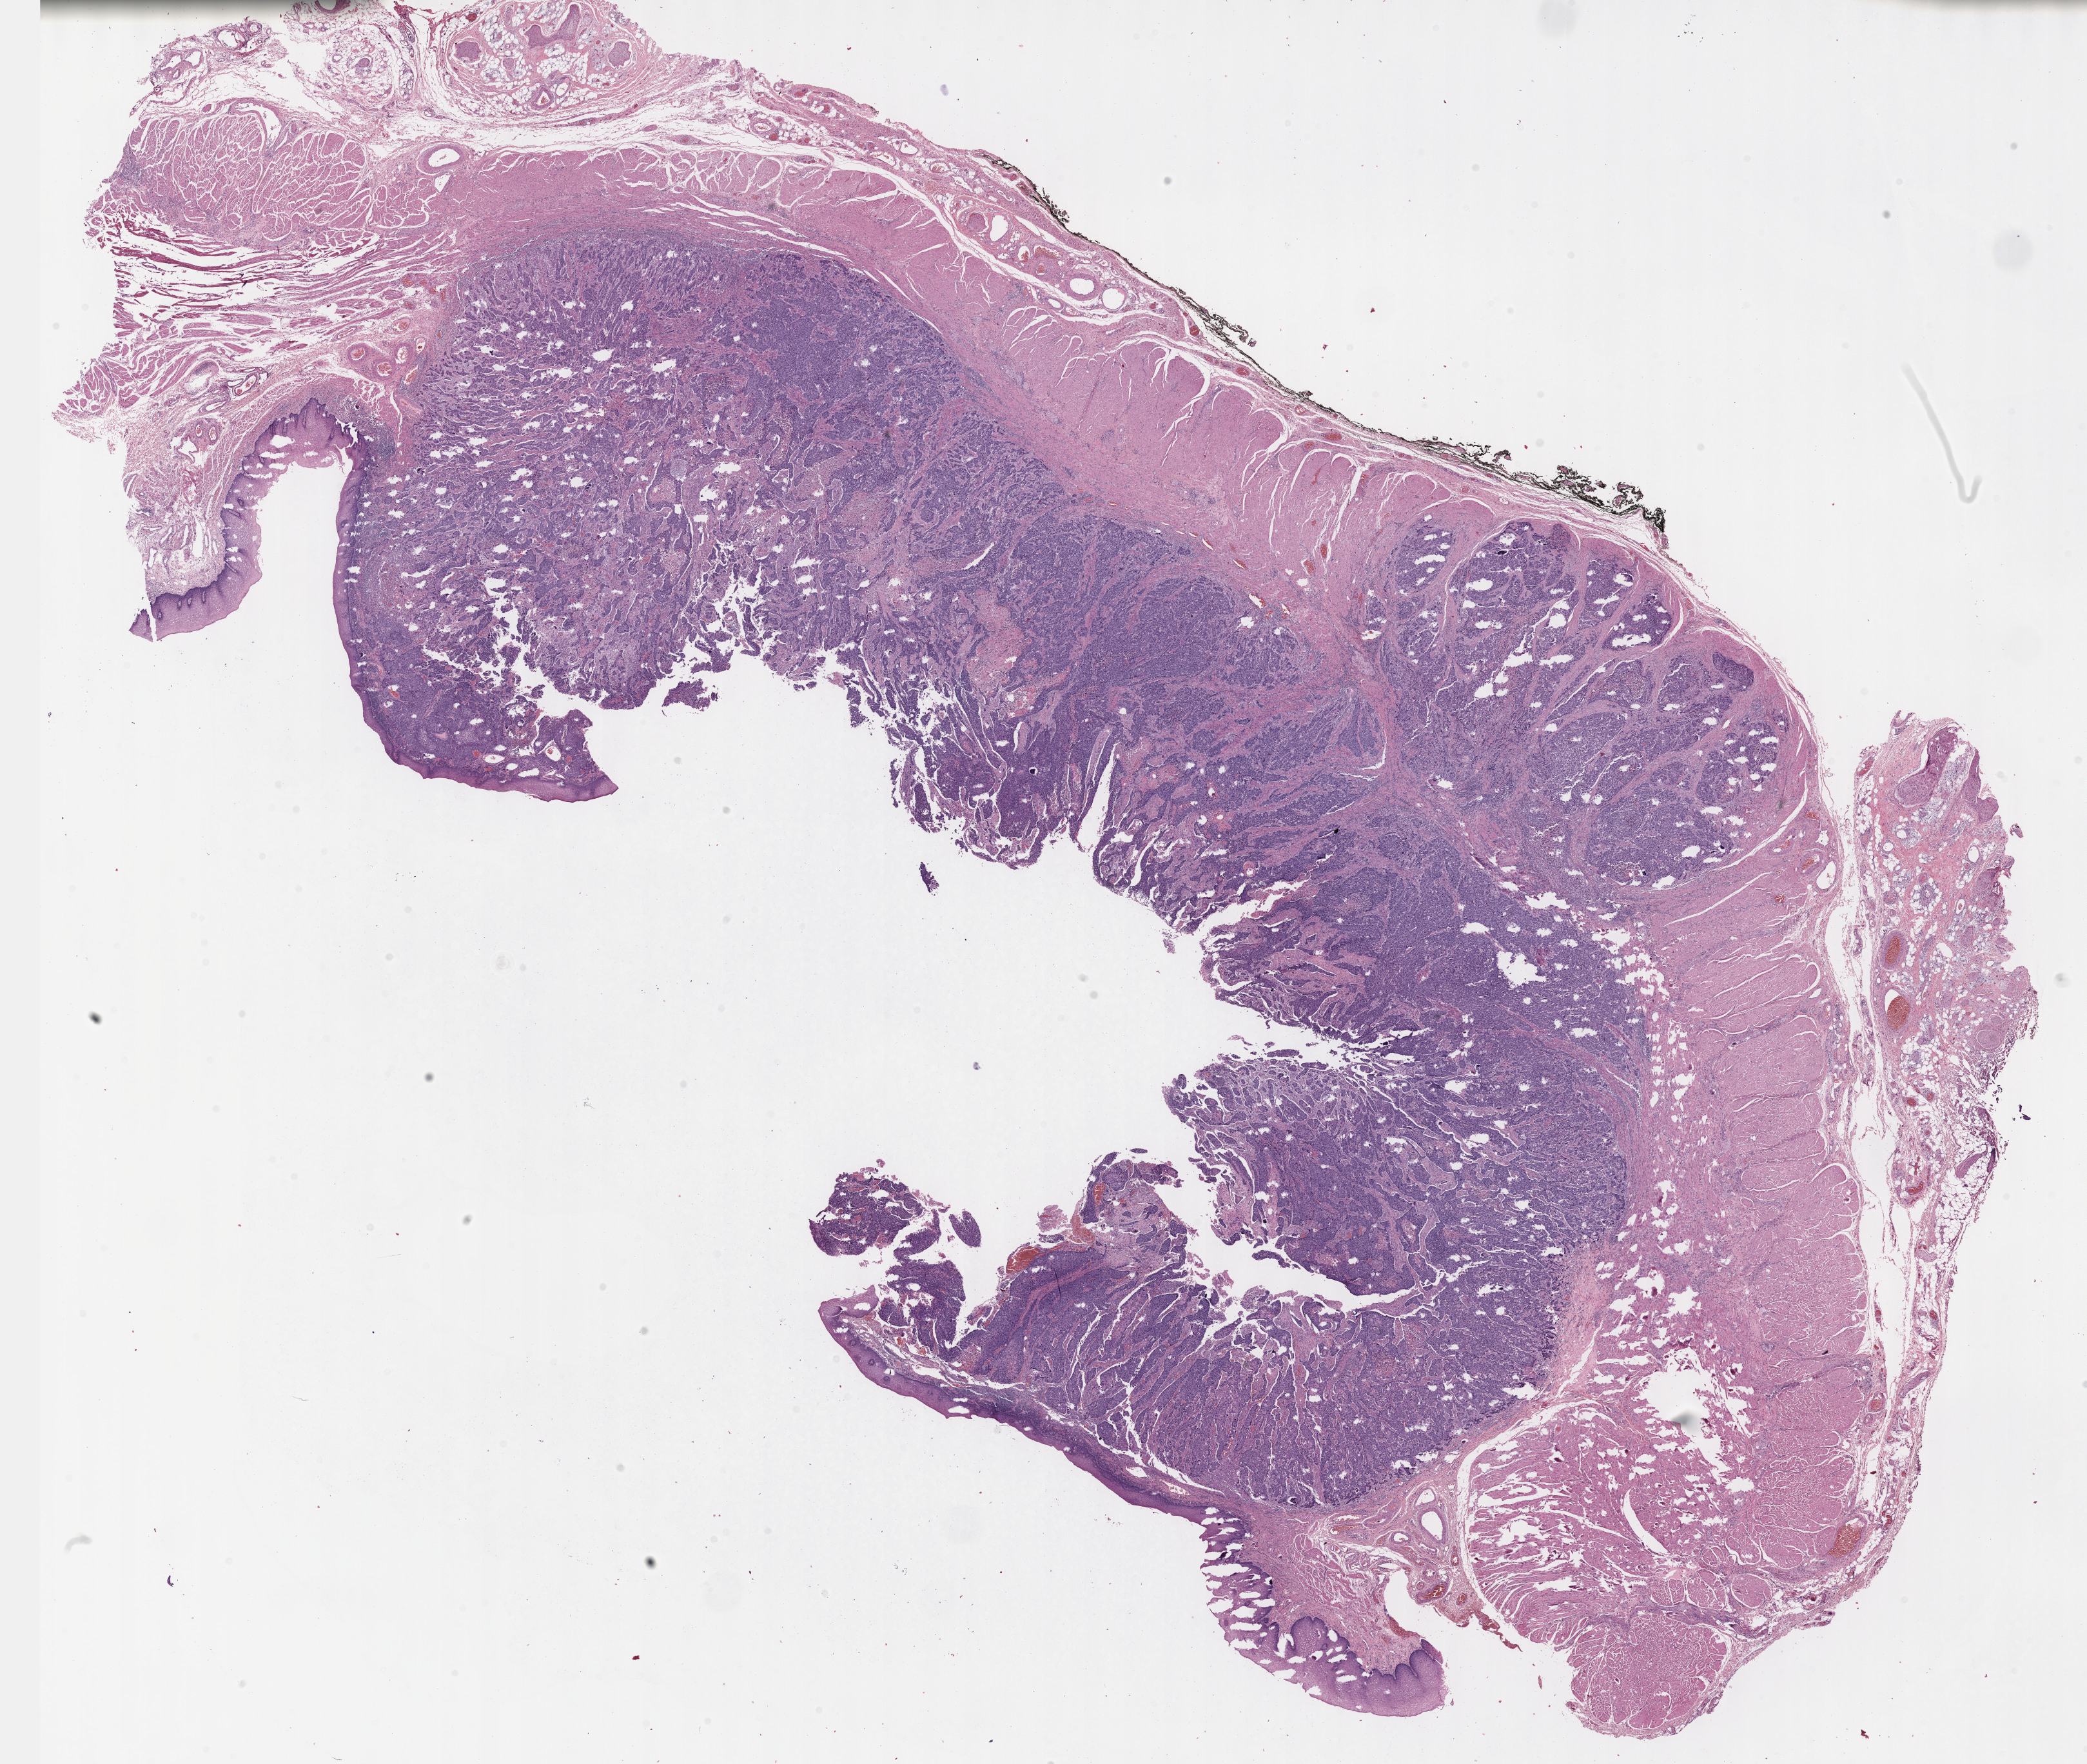
Whole-slide histology image, H&E, a low-resolution overview of the entire scanned area, about 26.2 x 22.1 mm; formalin-fixed paraffin-embedded (FFPE) diagnostic section; primary tumour sample from the esophagus. Patient: male, age at initial diagnosis 47 years. Histologic grade: G2 (moderately differentiated).
AJCC pathologic stage: IIIC (7th edition). Pathologic diagnosis: Squamous cell carcinoma, NOS (lower third of esophagus).